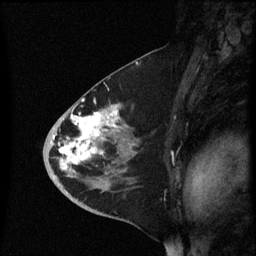
Breast MRI (dynamic contrast-enhanced), one sagittal slice; slice 34 of 60 in the series (ordered by position); dynamic contrast-enhanced series, image 2 of 3 at this slice position (ordered by acquisition); 1.5 T; TE 4.2 ms, TR 8.4 ms; 2.3 mm slice thickness; 256 × 256 image matrix. Female patient, age 46 years. Case-level facts recorded for this patient, not image findings: setting: breast cancer imaged before/during neoadjuvant chemotherapy; receptor status: HER2-positive.
Annotated regions visible in this slice (semi-automatically segmented with operator editing):
- analysis volume of interest (the breast-tissue region the enhancement analysis was run in; not a lesion): bounding box [x1, y1, x2, y2] px = [44, 96, 139, 187]
- tumour enhancement mask (voxels above the 70 % enhancement threshold inside the analysis volume of interest): [53, 106, 120, 173]